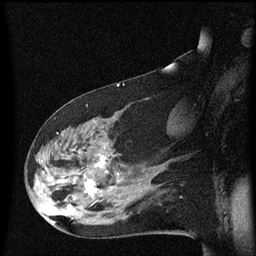
Breast MRI (dynamic contrast-enhanced), one sagittal slice; position 34 of 60 along the scan axis; dynamic contrast-enhanced series, image 2 of 3 at this slice position (ordered by acquisition); 1.5 T; TE 4.2 ms, TR 8.4 ms; 256 × 256 image matrix, field of view 200 × 200 mm. Female patient, age 48 years.
Outlined on this slice (semi-automatic segmentation, software-assisted and operator-edited):
- analysis volume of interest (the breast-tissue region the enhancement analysis was run in; not a lesion): bounding box [x1, y1, x2, y2] px = [31, 116, 134, 225]
- tumour enhancement mask (voxels above the 70 % enhancement threshold inside the analysis volume of interest): [84, 156, 118, 197]